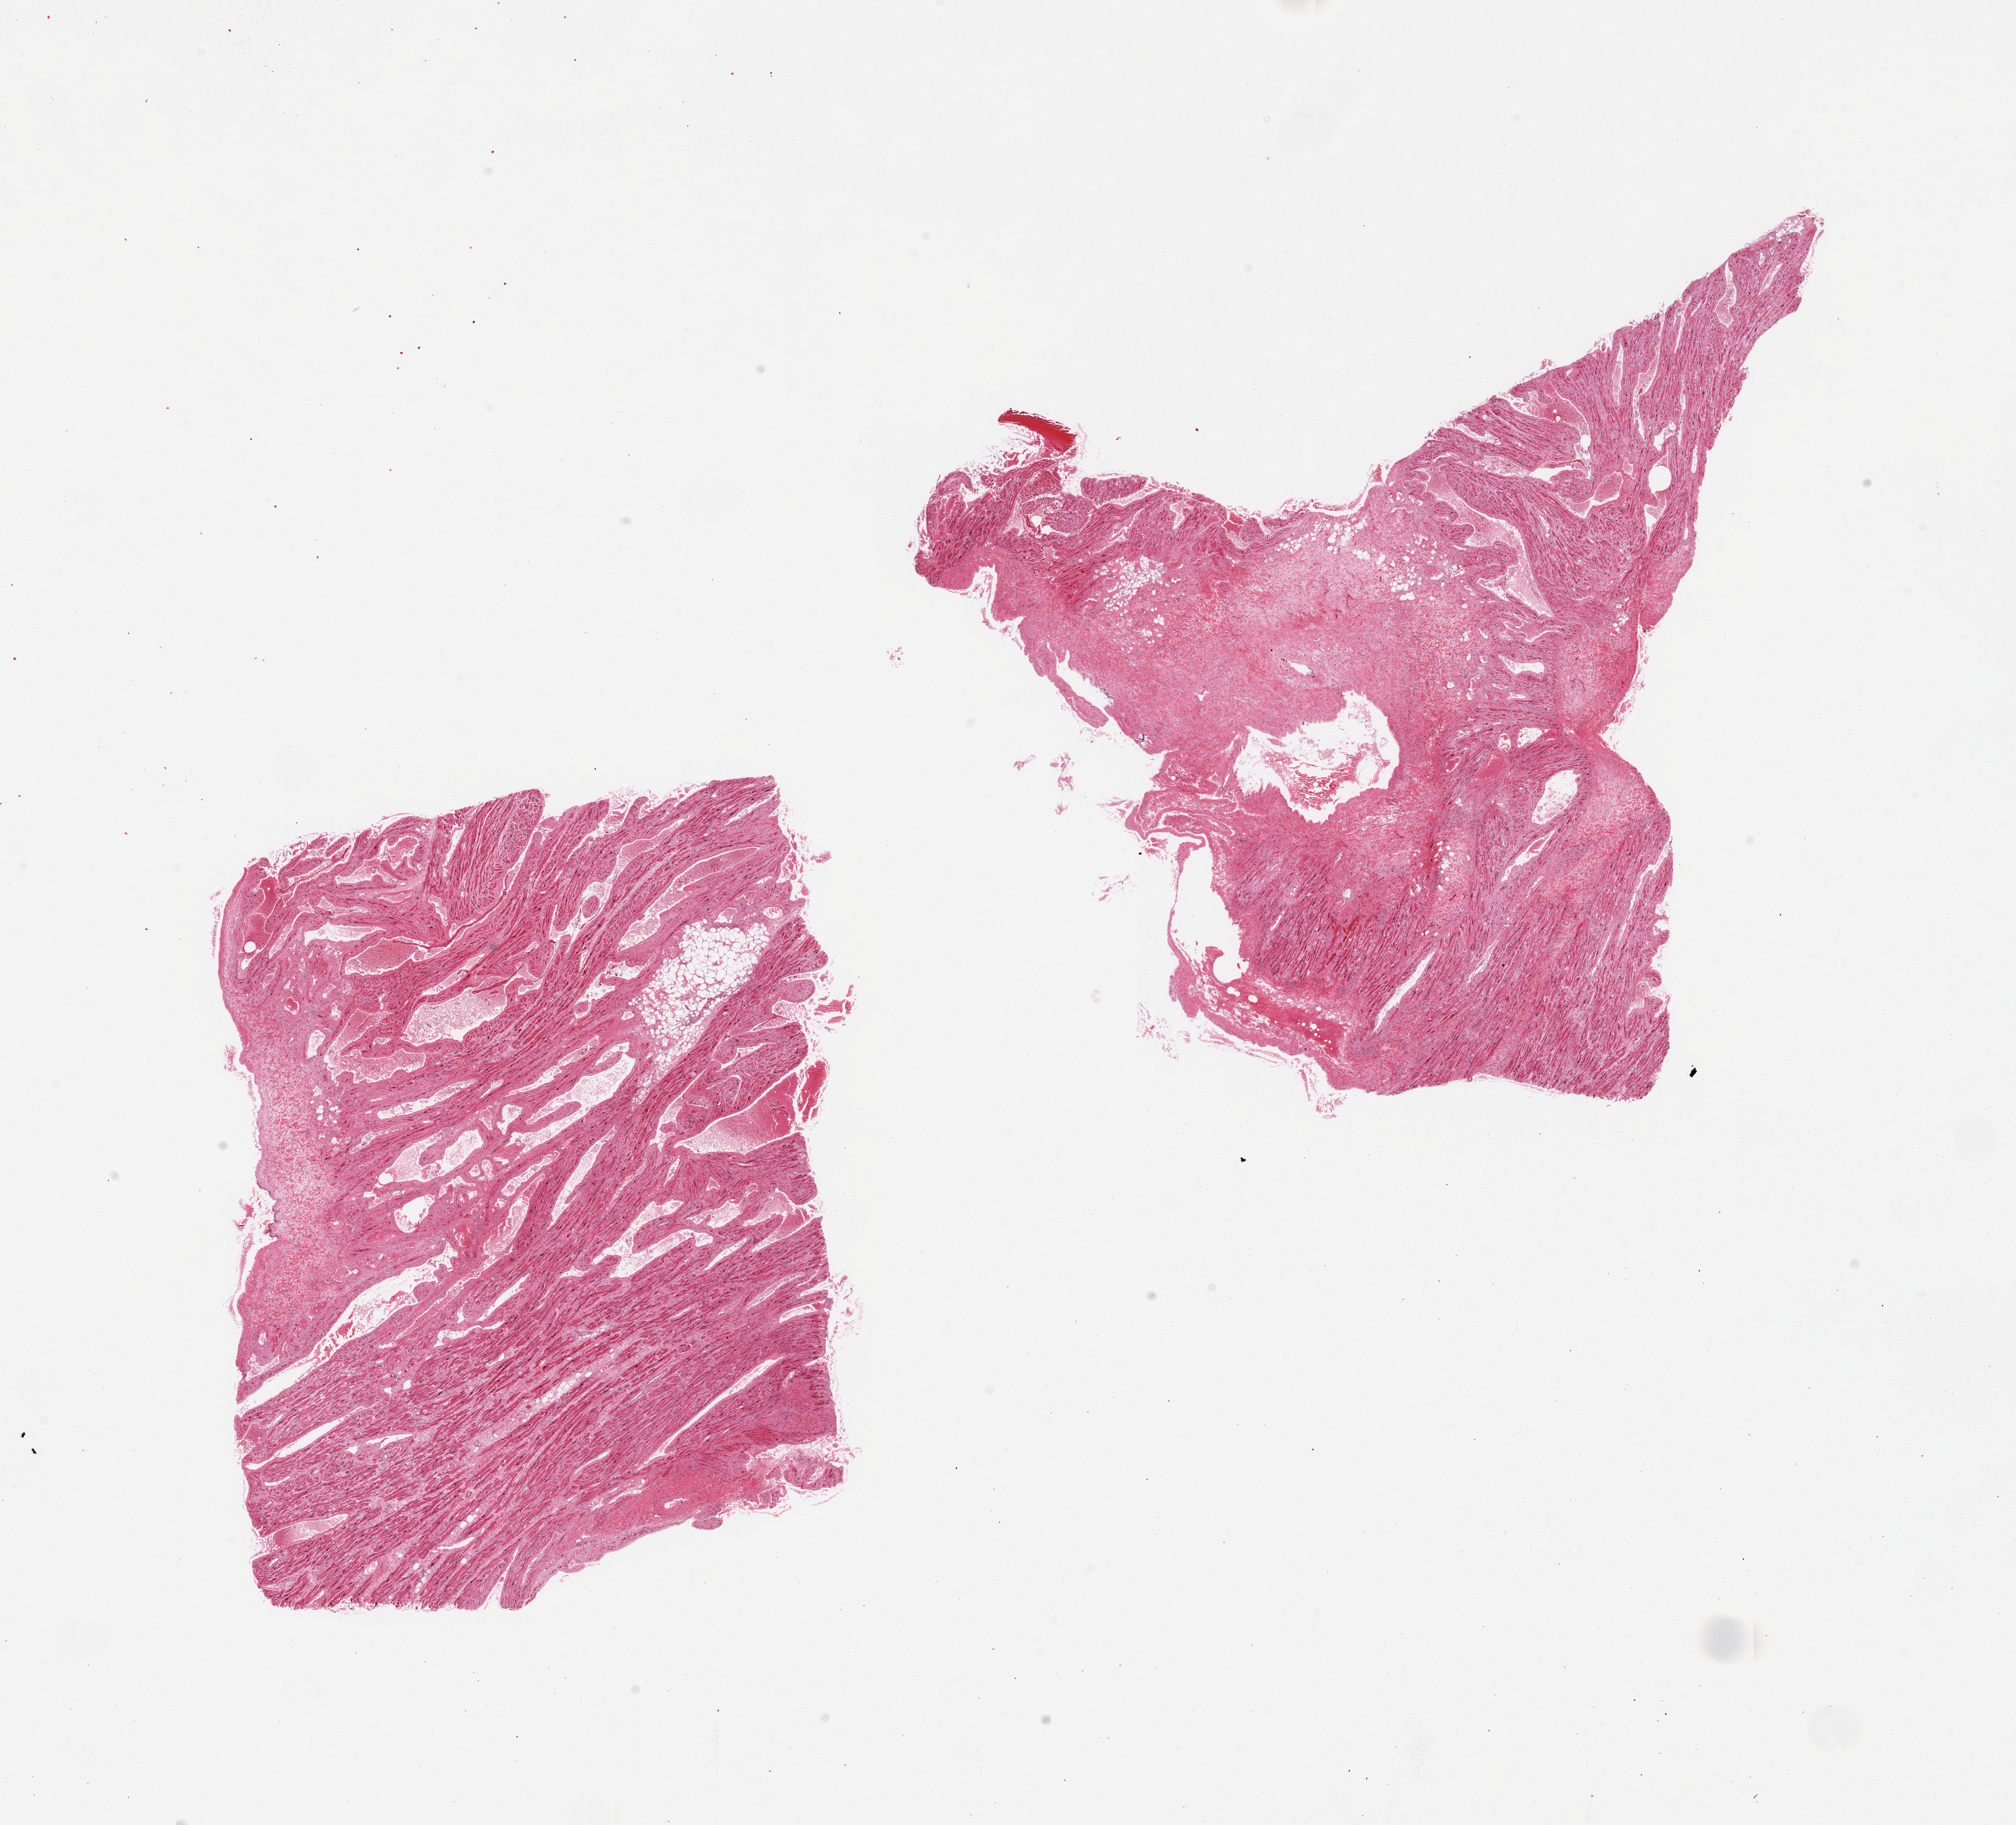
Hematoxylin and eosin (H&E) whole-slide image, brightfield — whole scanned area (about 22.6 x 20.5 mm) shown as a low-resolution overview, PAXgene-fixed paraffin-embedded (PFPE) section, target tissue: auricular appendage, donor tissue sample. Donor sex: female.
Review note (as recorded): 2 pieces; 30 & 40% fibrous component.